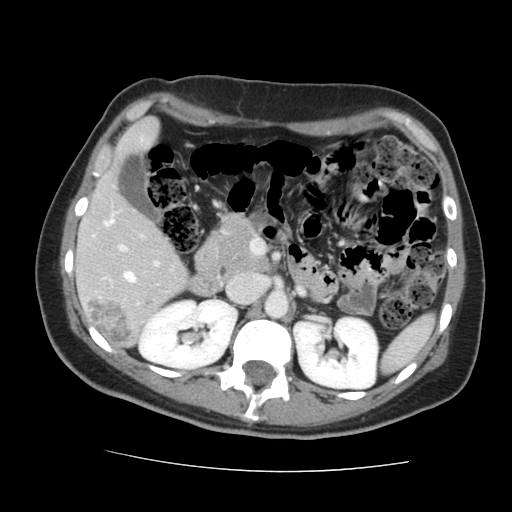
Contrast-enhanced abdominal CT, one axial slice; slice 79 of 144 in the series (ordered by position); 120 kVp; intravenous contrast given; soft-tissue window (W 400 / L 40 HU); 2.5 mm slice thickness; 512 × 512 image matrix. Female patient, age 46 years. From the clinical record (not read from this slice): diagnosis: colorectal cancer liver metastases, imaged before liver resection; multiple liver metastases: no; largest metastasis: 2.8 cm.
Structures marked on this image (manually delineated by an expert):
- liver: bounding box (x1, y1, x2, y2) in pixels: (78, 121, 188, 346)
- planned liver remnant (the part of the liver to remain after resection): (78, 121, 188, 336)
- portal vein (with intrahepatic branches): (104, 220, 158, 282)
- liver metastasis: (90, 295, 135, 344)